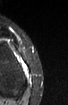
MRI of an extremity soft-tissue mass, one axial slice. Slice 18 of 52 in the series (ordered by position). STIR. MR volume resampled by the dataset authors to the PET/CT grid (not the native acquisition matrix). 3.27 mm slice thickness. 68 × 105 image matrix, field of view 66 × 103 mm. Female patient. From the clinical record (not read from this slice): histological type: spindle cell suggestive of biphasic synovial sarcoma; grade: intermediate; site of the primary tumour: left knee.
Structures marked on this image (expert contour drawn on MRI and transferred to this co-registered scan by the dataset authors):
- gross tumour volume including surrounding oedema: bounding box (x1, y1, x2, y2) in pixels: (21, 63, 27, 71)